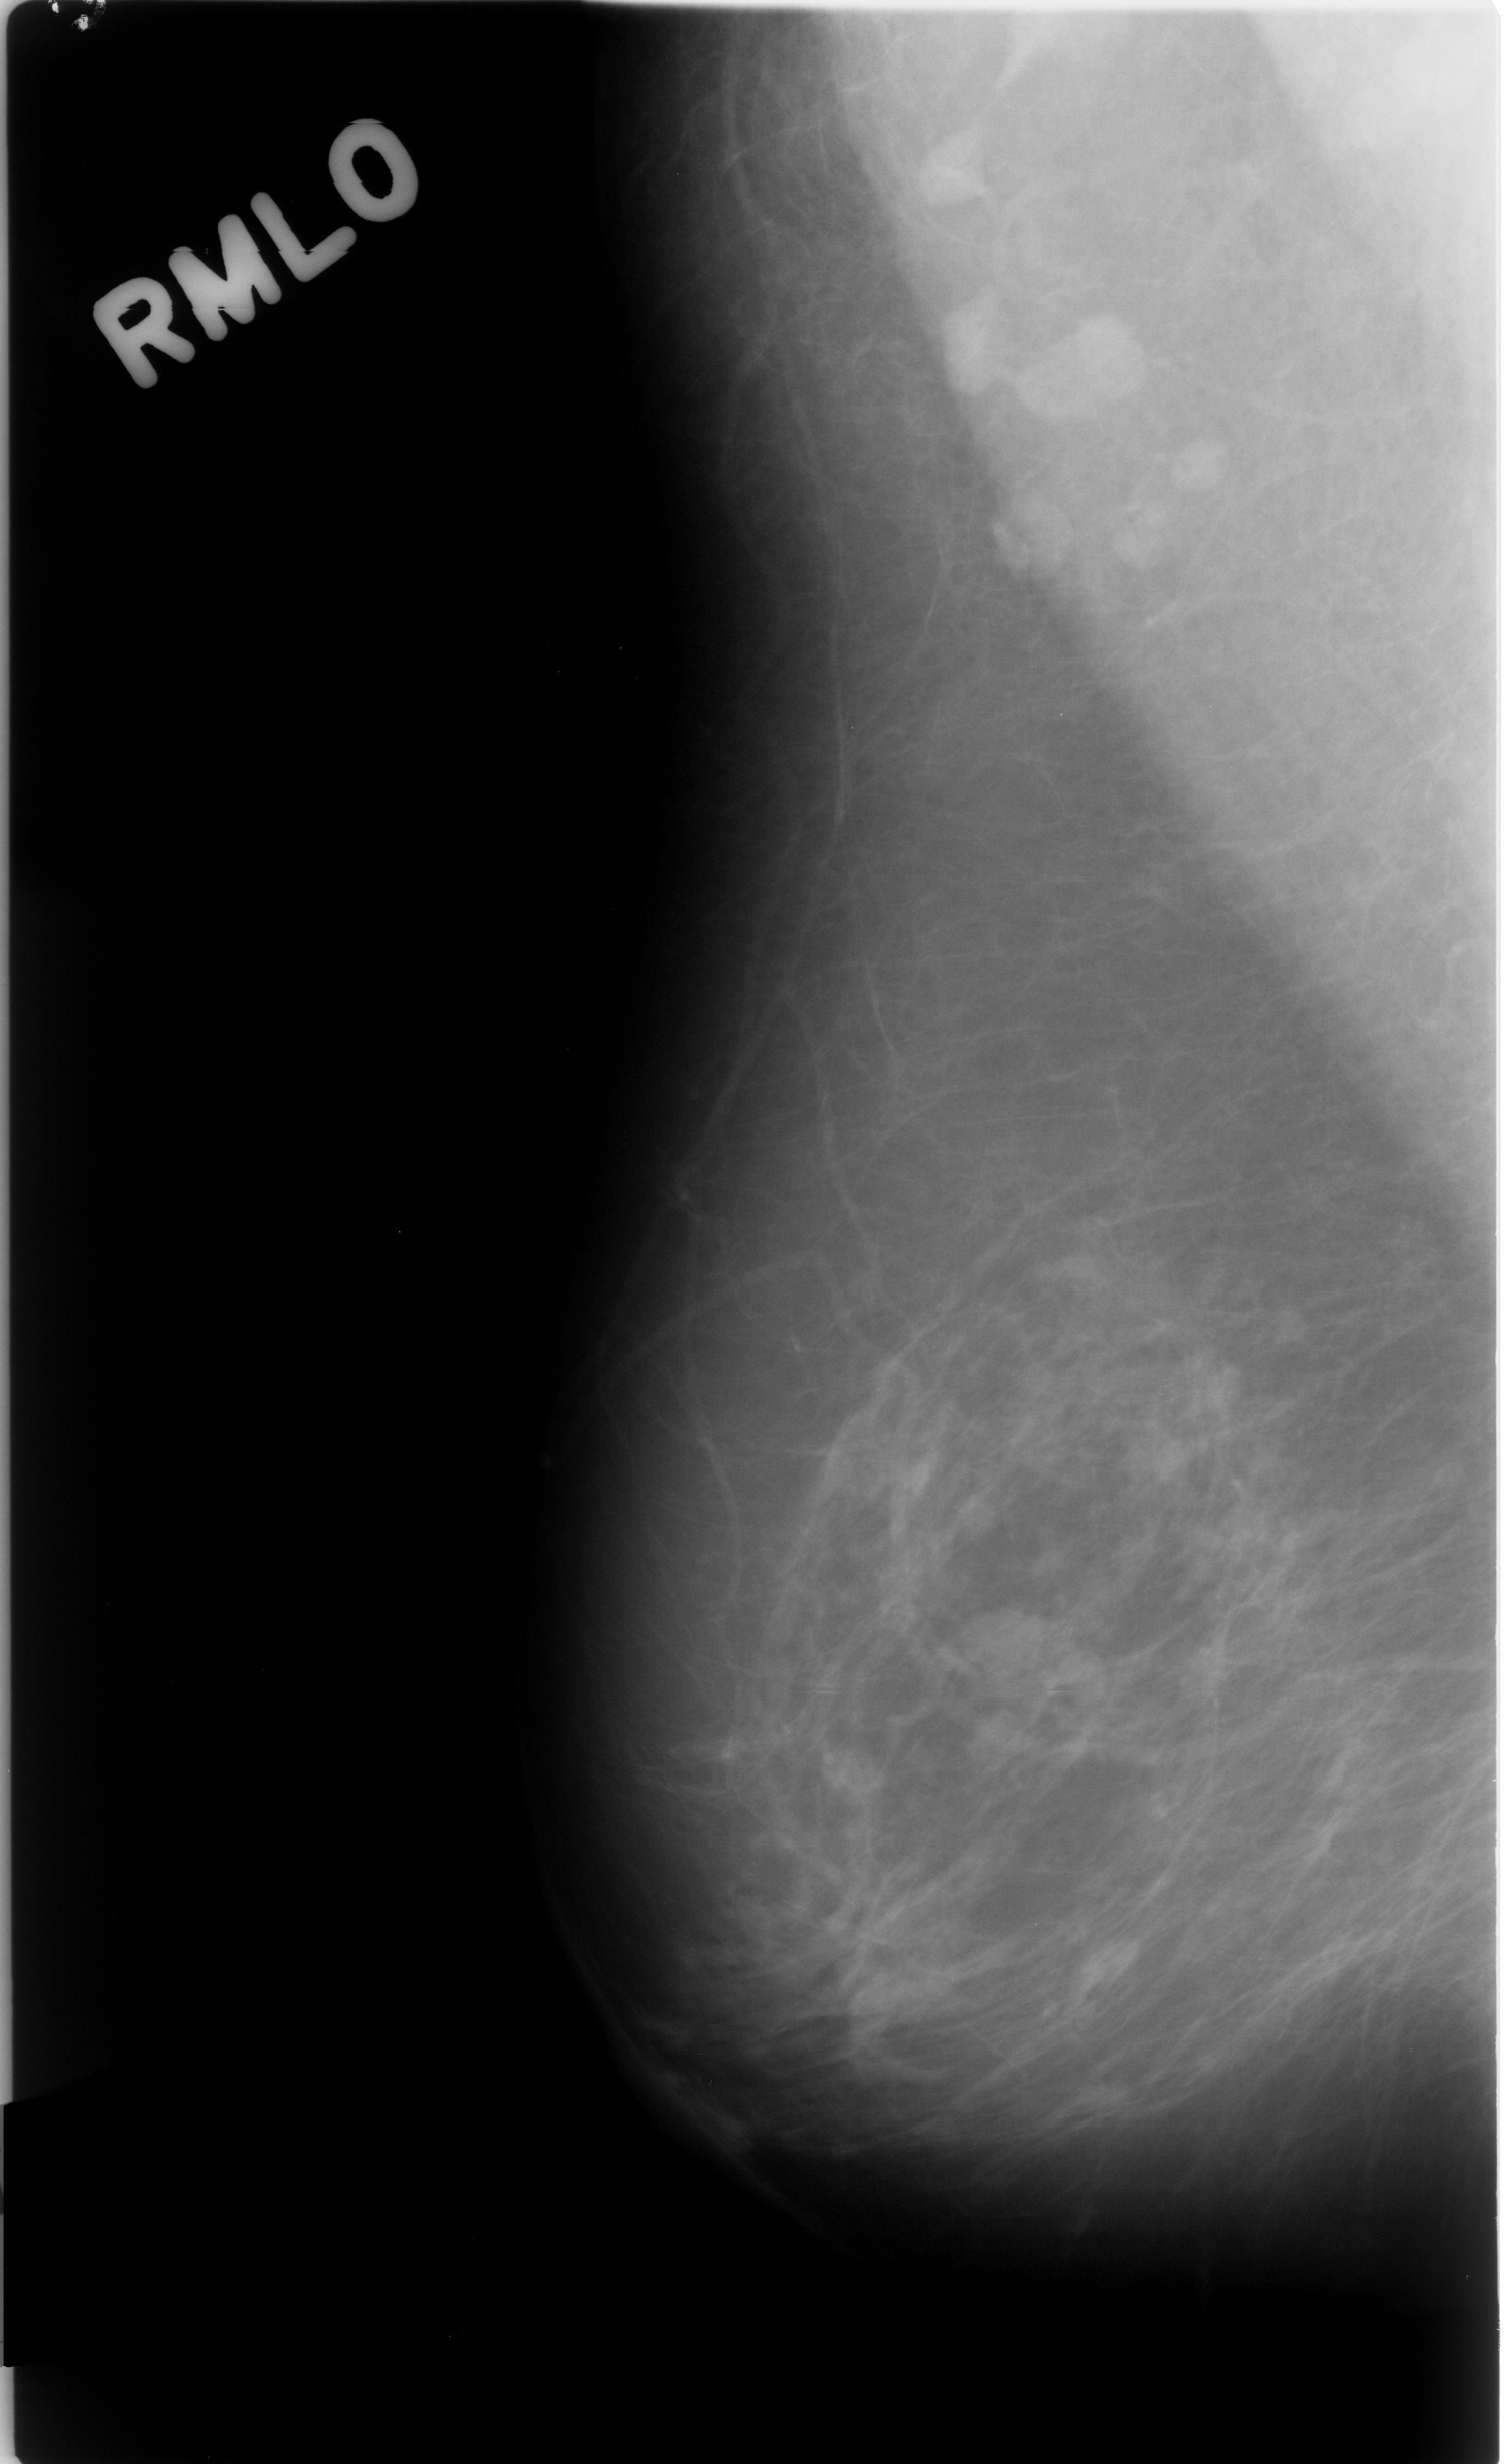
Scanned film-screen mammogram; right breast; MLO view; breast composition: almost entirely fatty (BI-RADS density category 1 of 4).
- Mass, shape lobulated, margins circumscribed; BI-RADS assessment category 3; subtlety rating 4 on a 1 (subtle) to 5 (obvious) scale; benign without callback (not worked up further).